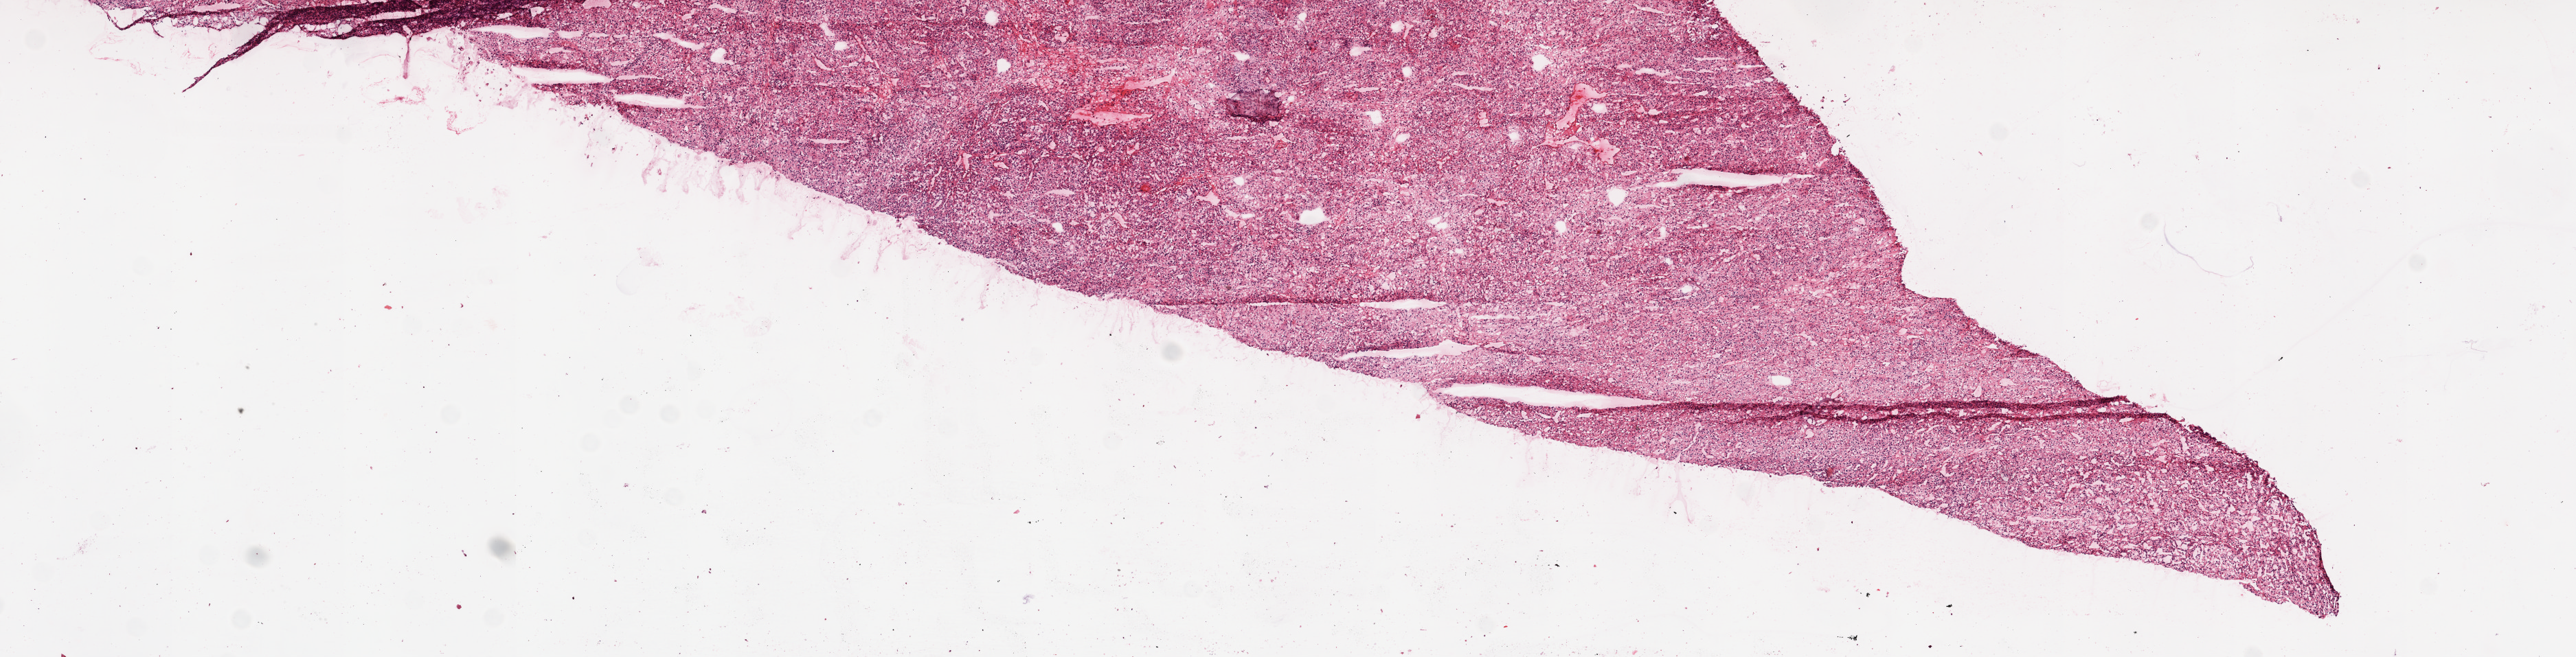
Whole-slide histology image, H&E-stained, shown as a low-resolution overview of the whole scanned area (about 15.0 x 3.8 mm); frozen section; primary tumour sample from the kidney. Female patient; age at initial diagnosis 69 years. Histologic grade: G3 (poorly differentiated). Composition of this section per pathologist review: tumour cells 95%, tumour nuclei 90%, normal cells 0%, stromal cells 5%, necrosis 0%.
AJCC pathologic stage: I. Diagnosis: Clear cell adenocarcinoma, NOS.